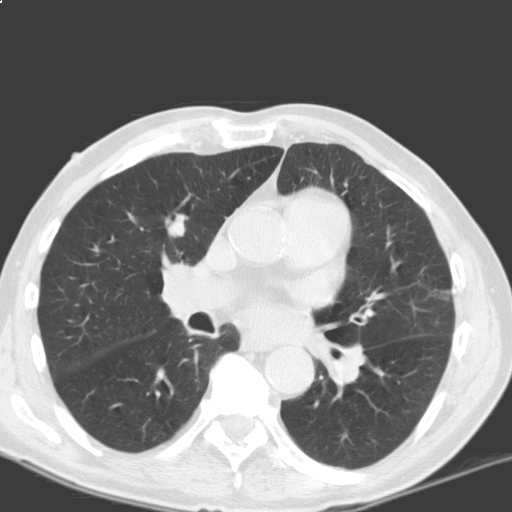
Axial slice from a low-dose chest CT screening exam; baseline annual screen; lung window (W 1500 / L -600 HU); standard (soft-tissue) reconstruction kernel (C); slice 87 of 184 in the series; 512 × 512 image matrix. Male participant, aged 69 years at enrolment.
Expert-annotated lung lesion, bounding box (x1, y1, x2, y2) in pixels: (148, 202, 206, 253). The exam's reader record, not a measurement of the box and not confirmed to be the same lesion: non-calcified nodule or mass ≥4 mm, left lower lobe, 5 × 5 mm, smooth margins, soft tissue attenuation. Note: the box lies in the patient's right hemithorax on this image, whereas the reader's record names the left lung; they may be different findings. Participant outcome: lung cancer diagnosed 317 days after this screen (after the second annual screen) — squamous cell carcinoma, NOS, right upper lobe, moderately differentiated (G2), stage IB (AJCC 6th edition), 40 mm at pathology.